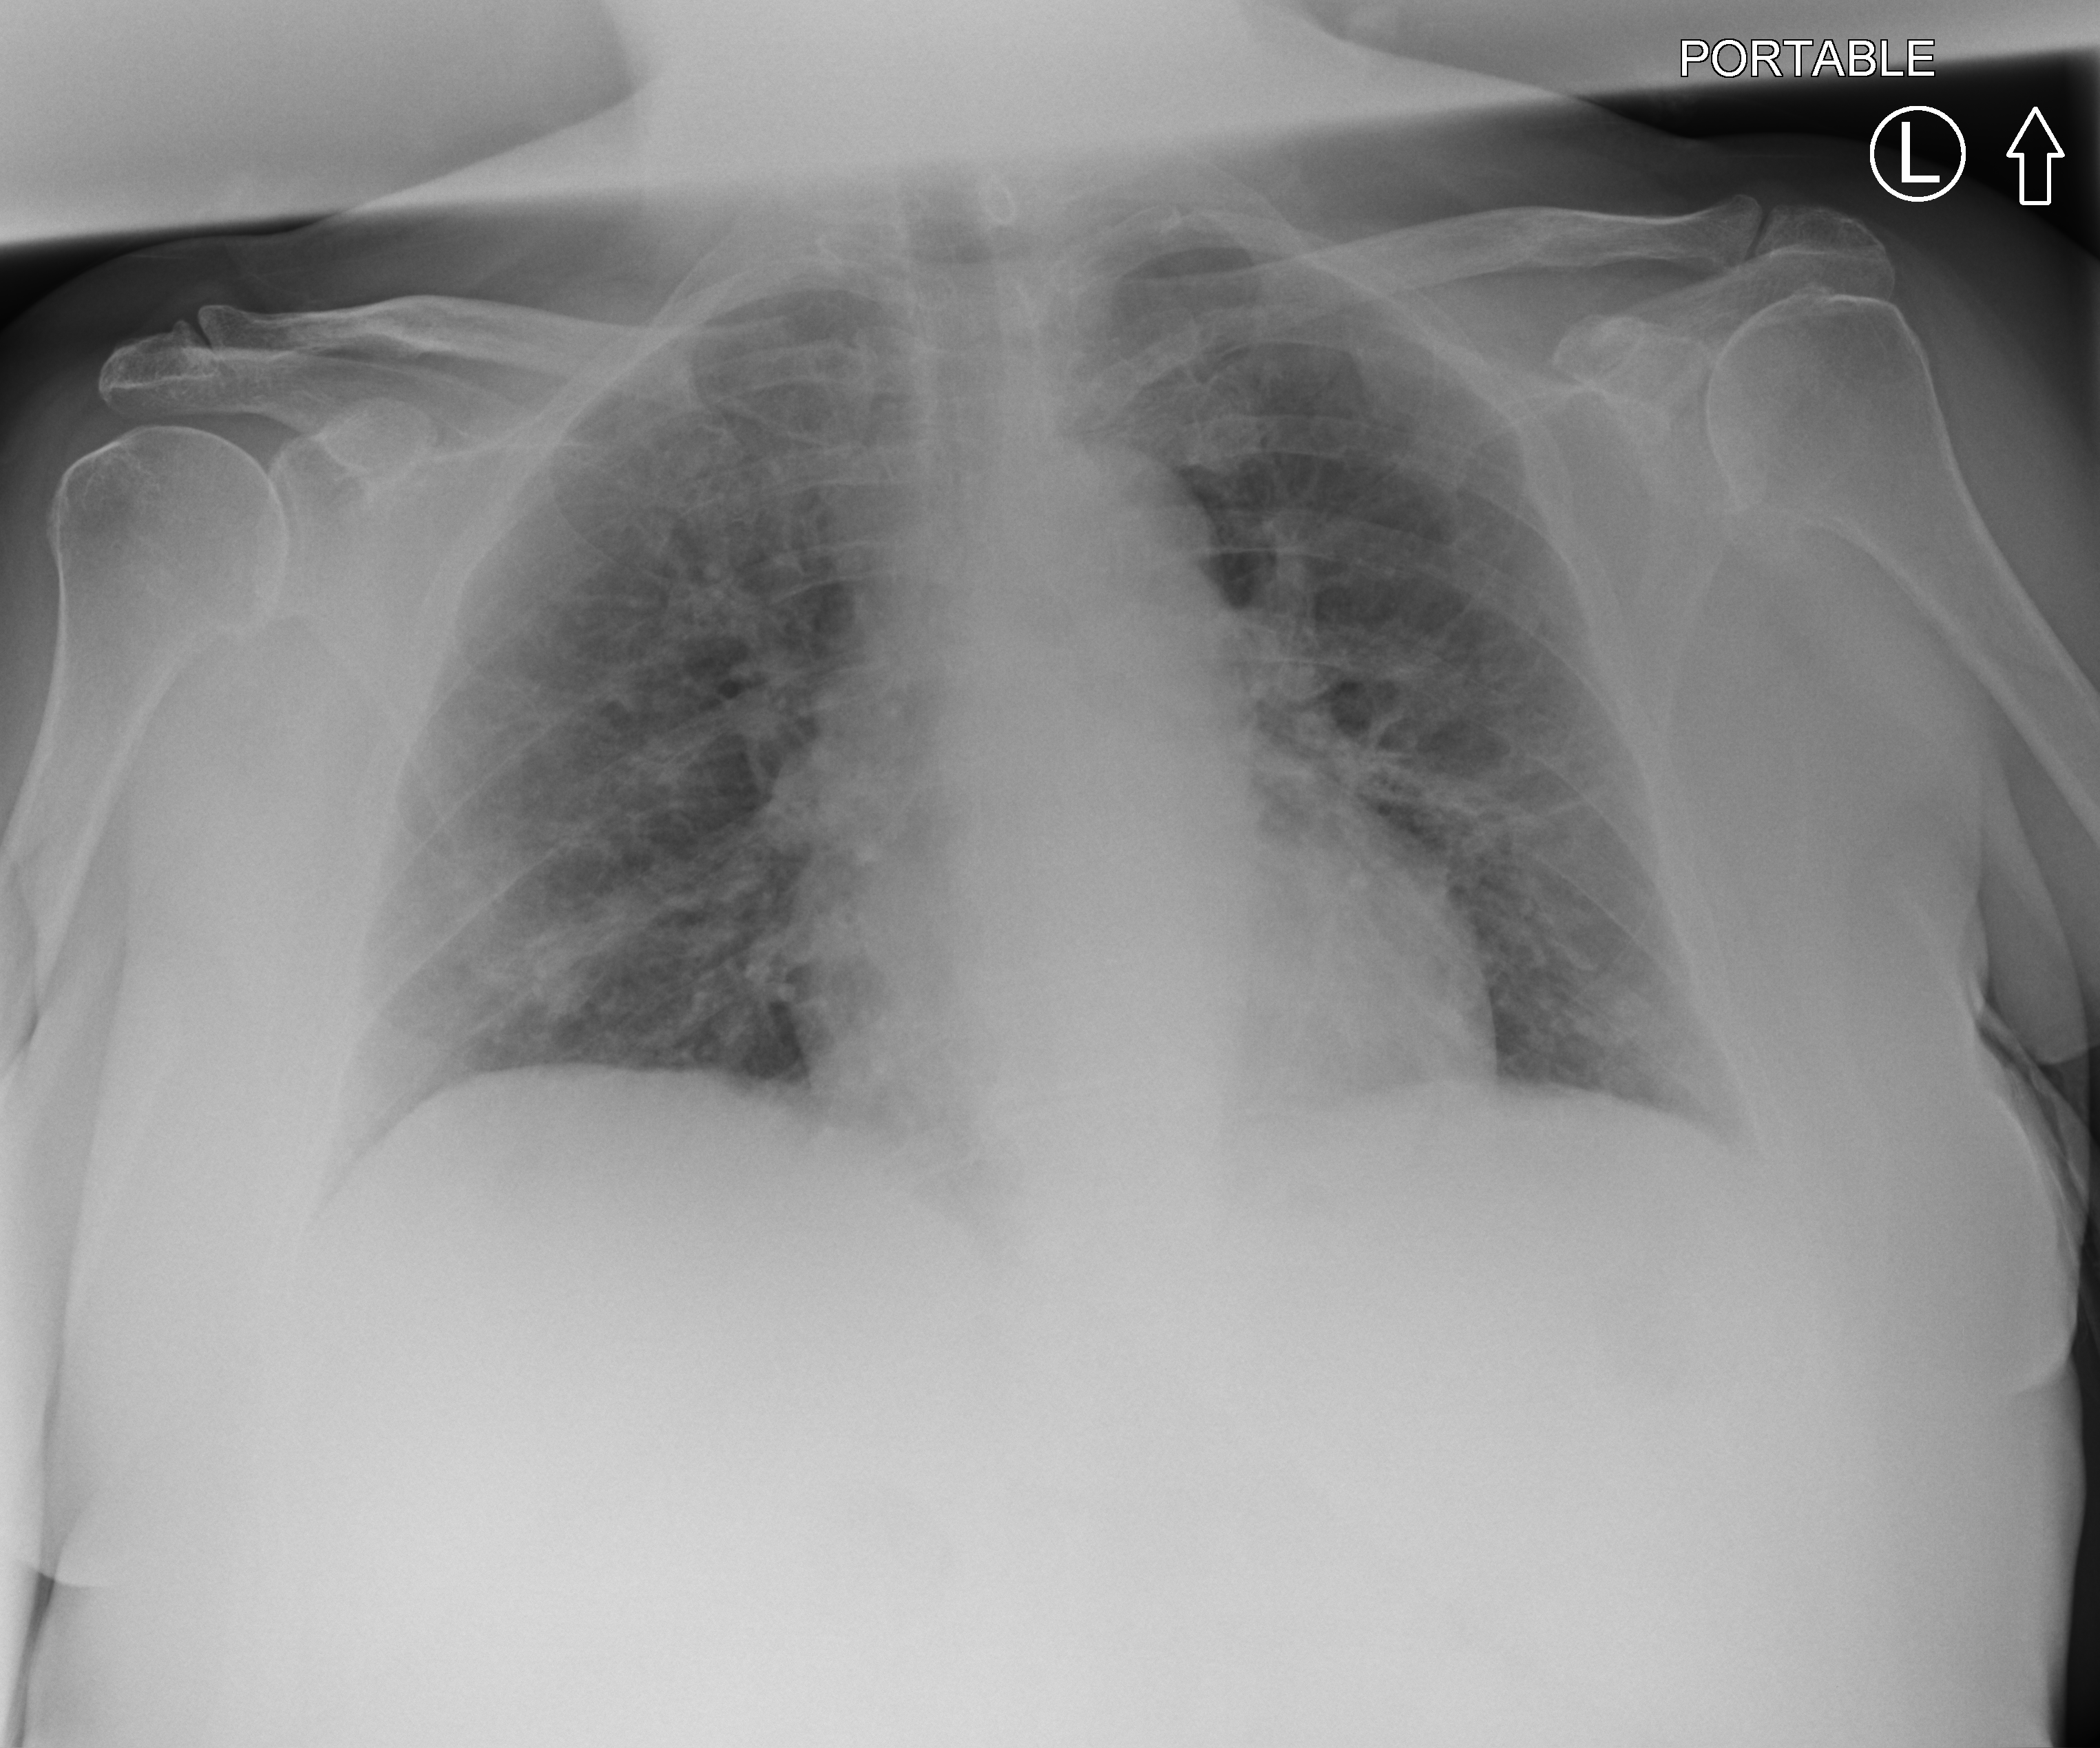
Chest X-ray, anteroposterior (AP) projection. Female patient hospitalised with COVID-19, age 60–74 years.
From the hospital-stay record, not from the radiograph (when in the stay this image was taken is not recorded):
- length of hospital stay: 6 days
- mechanically ventilated during this hospital stay: no